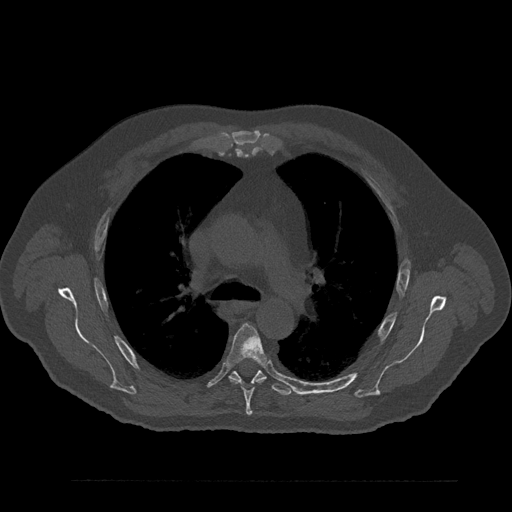
CT including the spine, one axial slice; slice 586 of 797 in the series (ordered by position); reconstruction kernel Br40s/3; 120 kVp; bone window (W 1800 / L 400 HU); 0.5 mm slice thickness; 512 × 512 image matrix, field of view 430 × 430 mm. Male patient, age 61 years. Case-level facts recorded for this patient, not image findings: primary cancer: prostate.
Structures marked on this image (semi-automatic segmentation, software-assisted and operator-edited):
- T5 vertebra: box from (x=227, y=324) to (x=266, y=416) px
- T6 vertebra: (x=229, y=363)–(x=292, y=396)